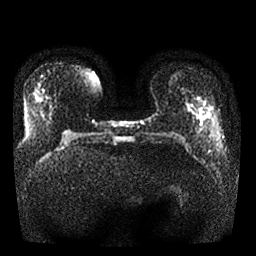
Breast MRI, one axial slice; diffusion-weighted series; image 2 of 4 stored at this slice position (different b-values; order by instance number); 1.5 T; 256 × 256 image matrix, field of view 340 × 340 mm. Female patient.
Structures marked on this image (manually delineated by an expert):
- tumour on diffusion-weighted imaging: bounding box (x1, y1, x2, y2) in pixels: (199, 116, 203, 121)